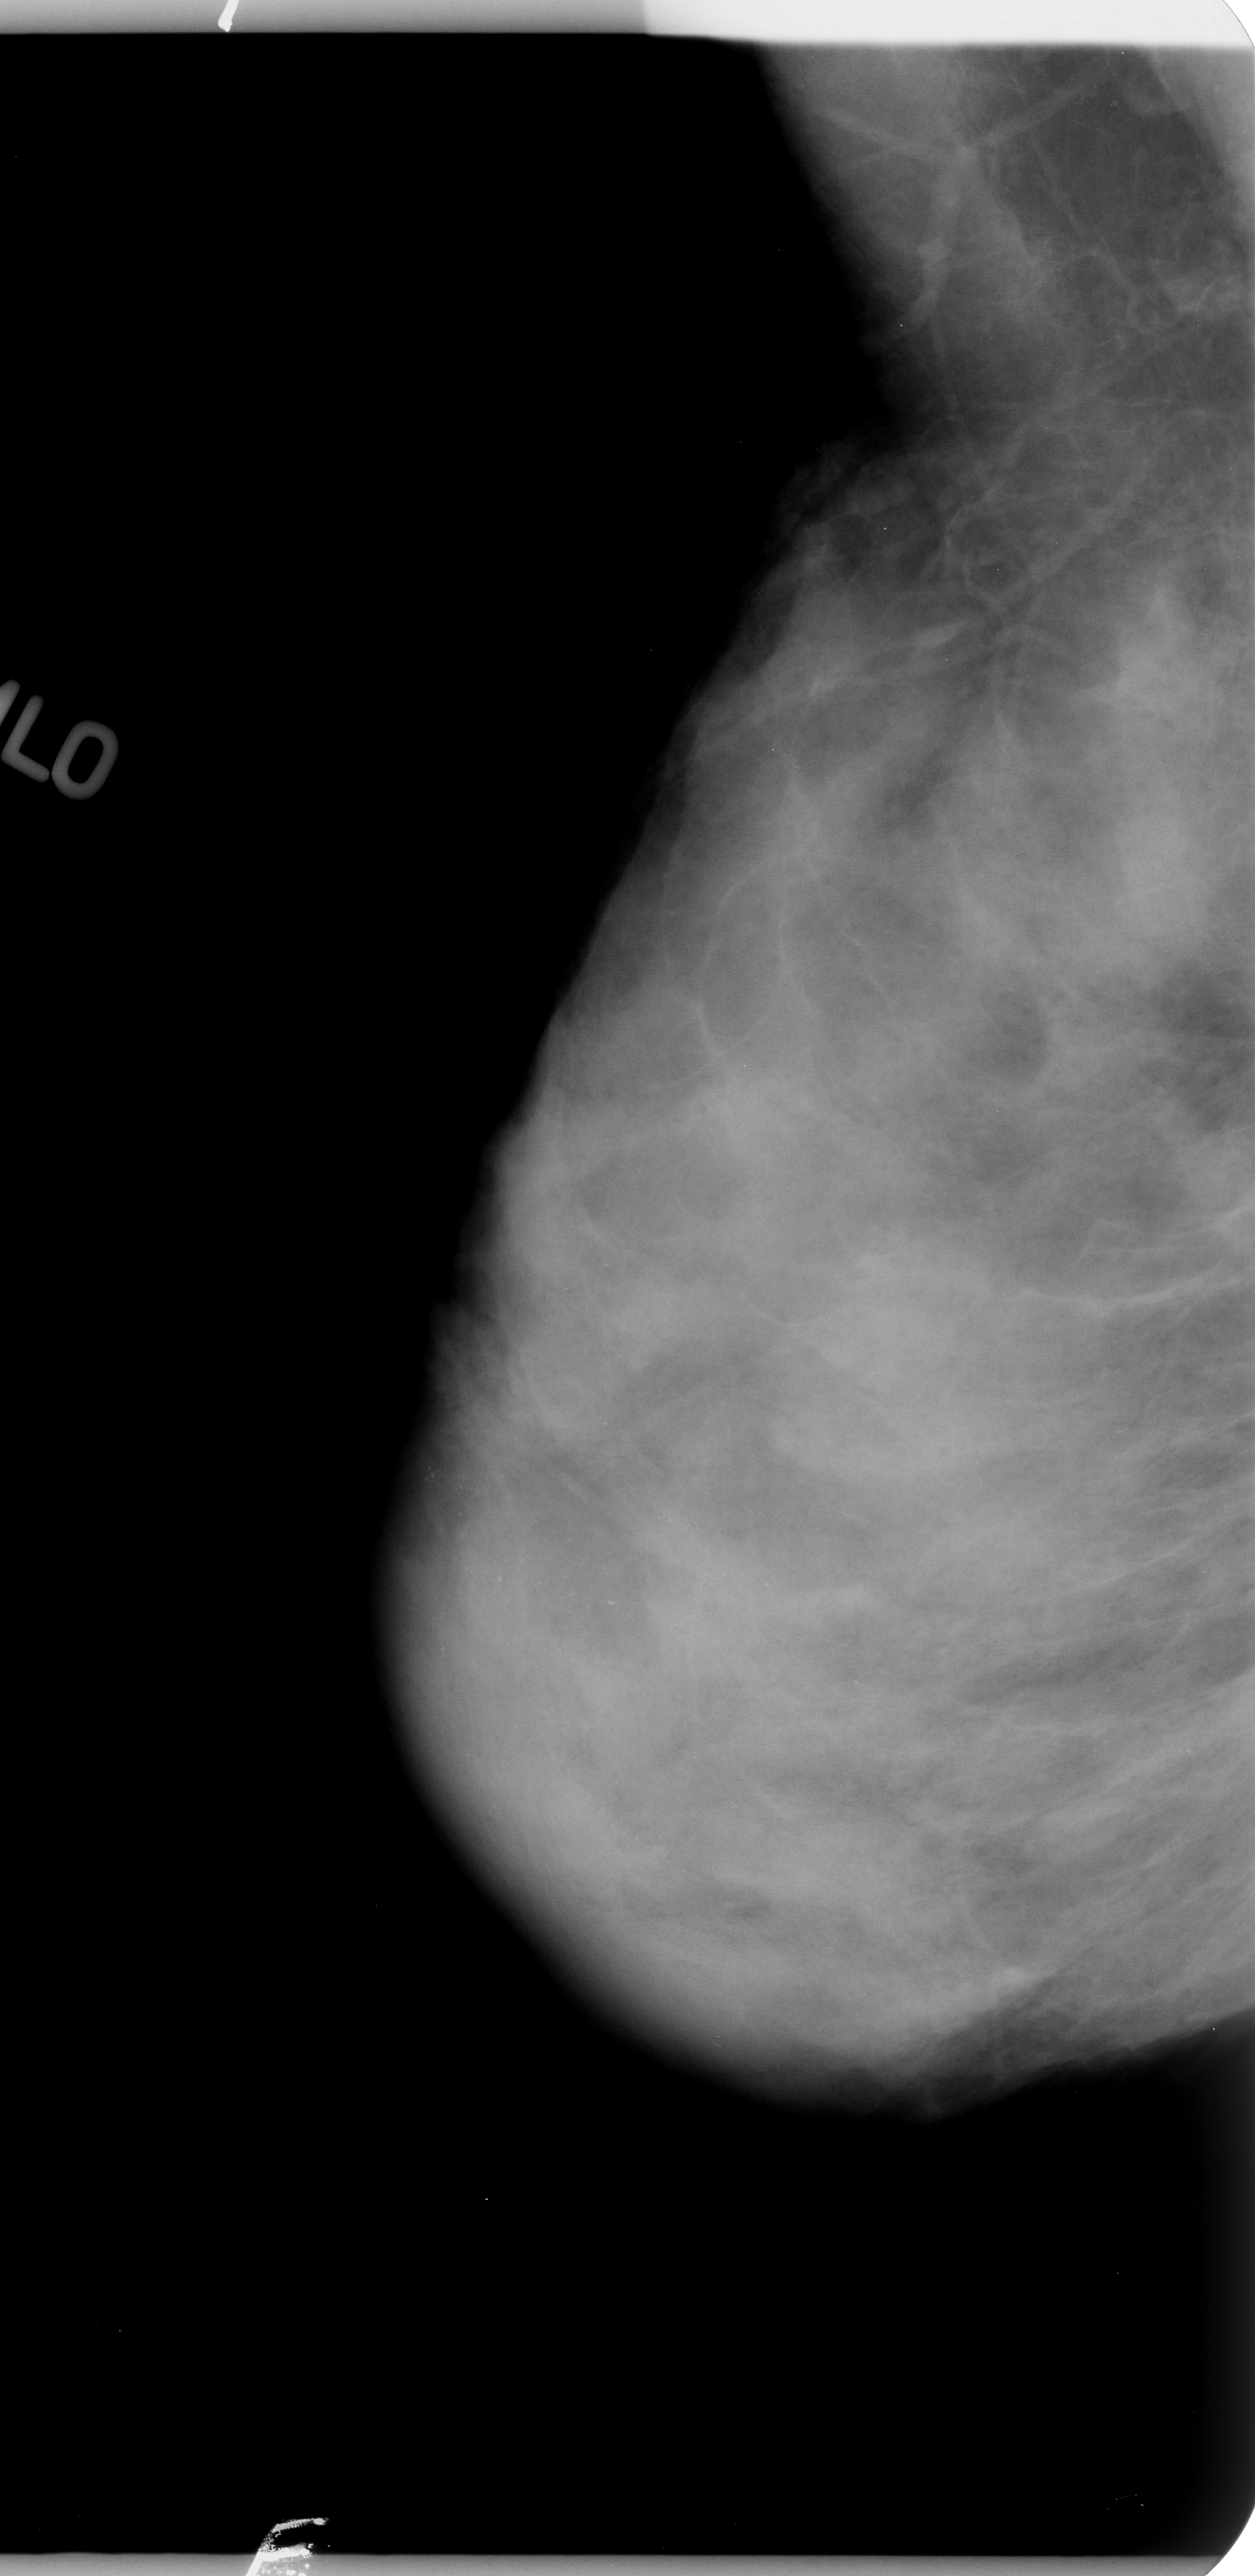
Mammogram (digitized film); right breast; mediolateral oblique (MLO) view; 1255 × 2576 image matrix.
Marked abnormalities (boxes around the expert regions of interest):
- calcifications, morphology pleomorphic, distribution regional; BI-RADS assessment category 4; pathology result (as recorded, not read from the image): benign: bounding box [x1, y1, x2, y2] px = [361, 1034, 979, 2040]